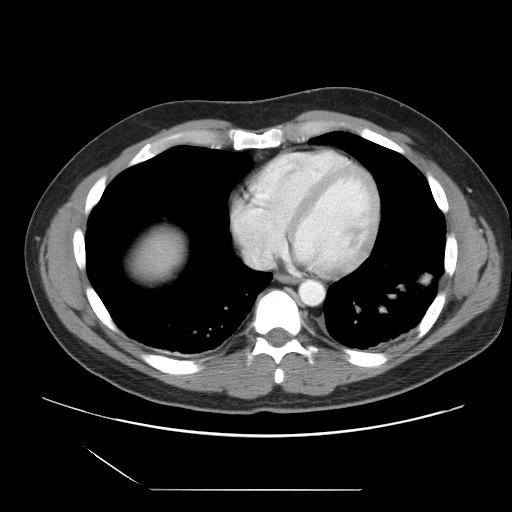
Contrast-enhanced abdominal CT, one axial slice; slice 34 of 39 in the series (ordered by position); intravenous contrast given; soft-tissue window (W 400 / L 40 HU); 5 mm slice thickness; 512 × 512 image matrix. Male patient, age 39 years. From the clinical record (not read from this slice): diagnosis: colorectal cancer liver metastases, imaged before liver resection; multiple liver metastases: yes; largest metastasis: 1.3 cm.
Outlined on this slice (outlined manually by an expert reader):
- liver: bounding box (x1, y1, x2, y2) in pixels: (130, 228, 183, 282)